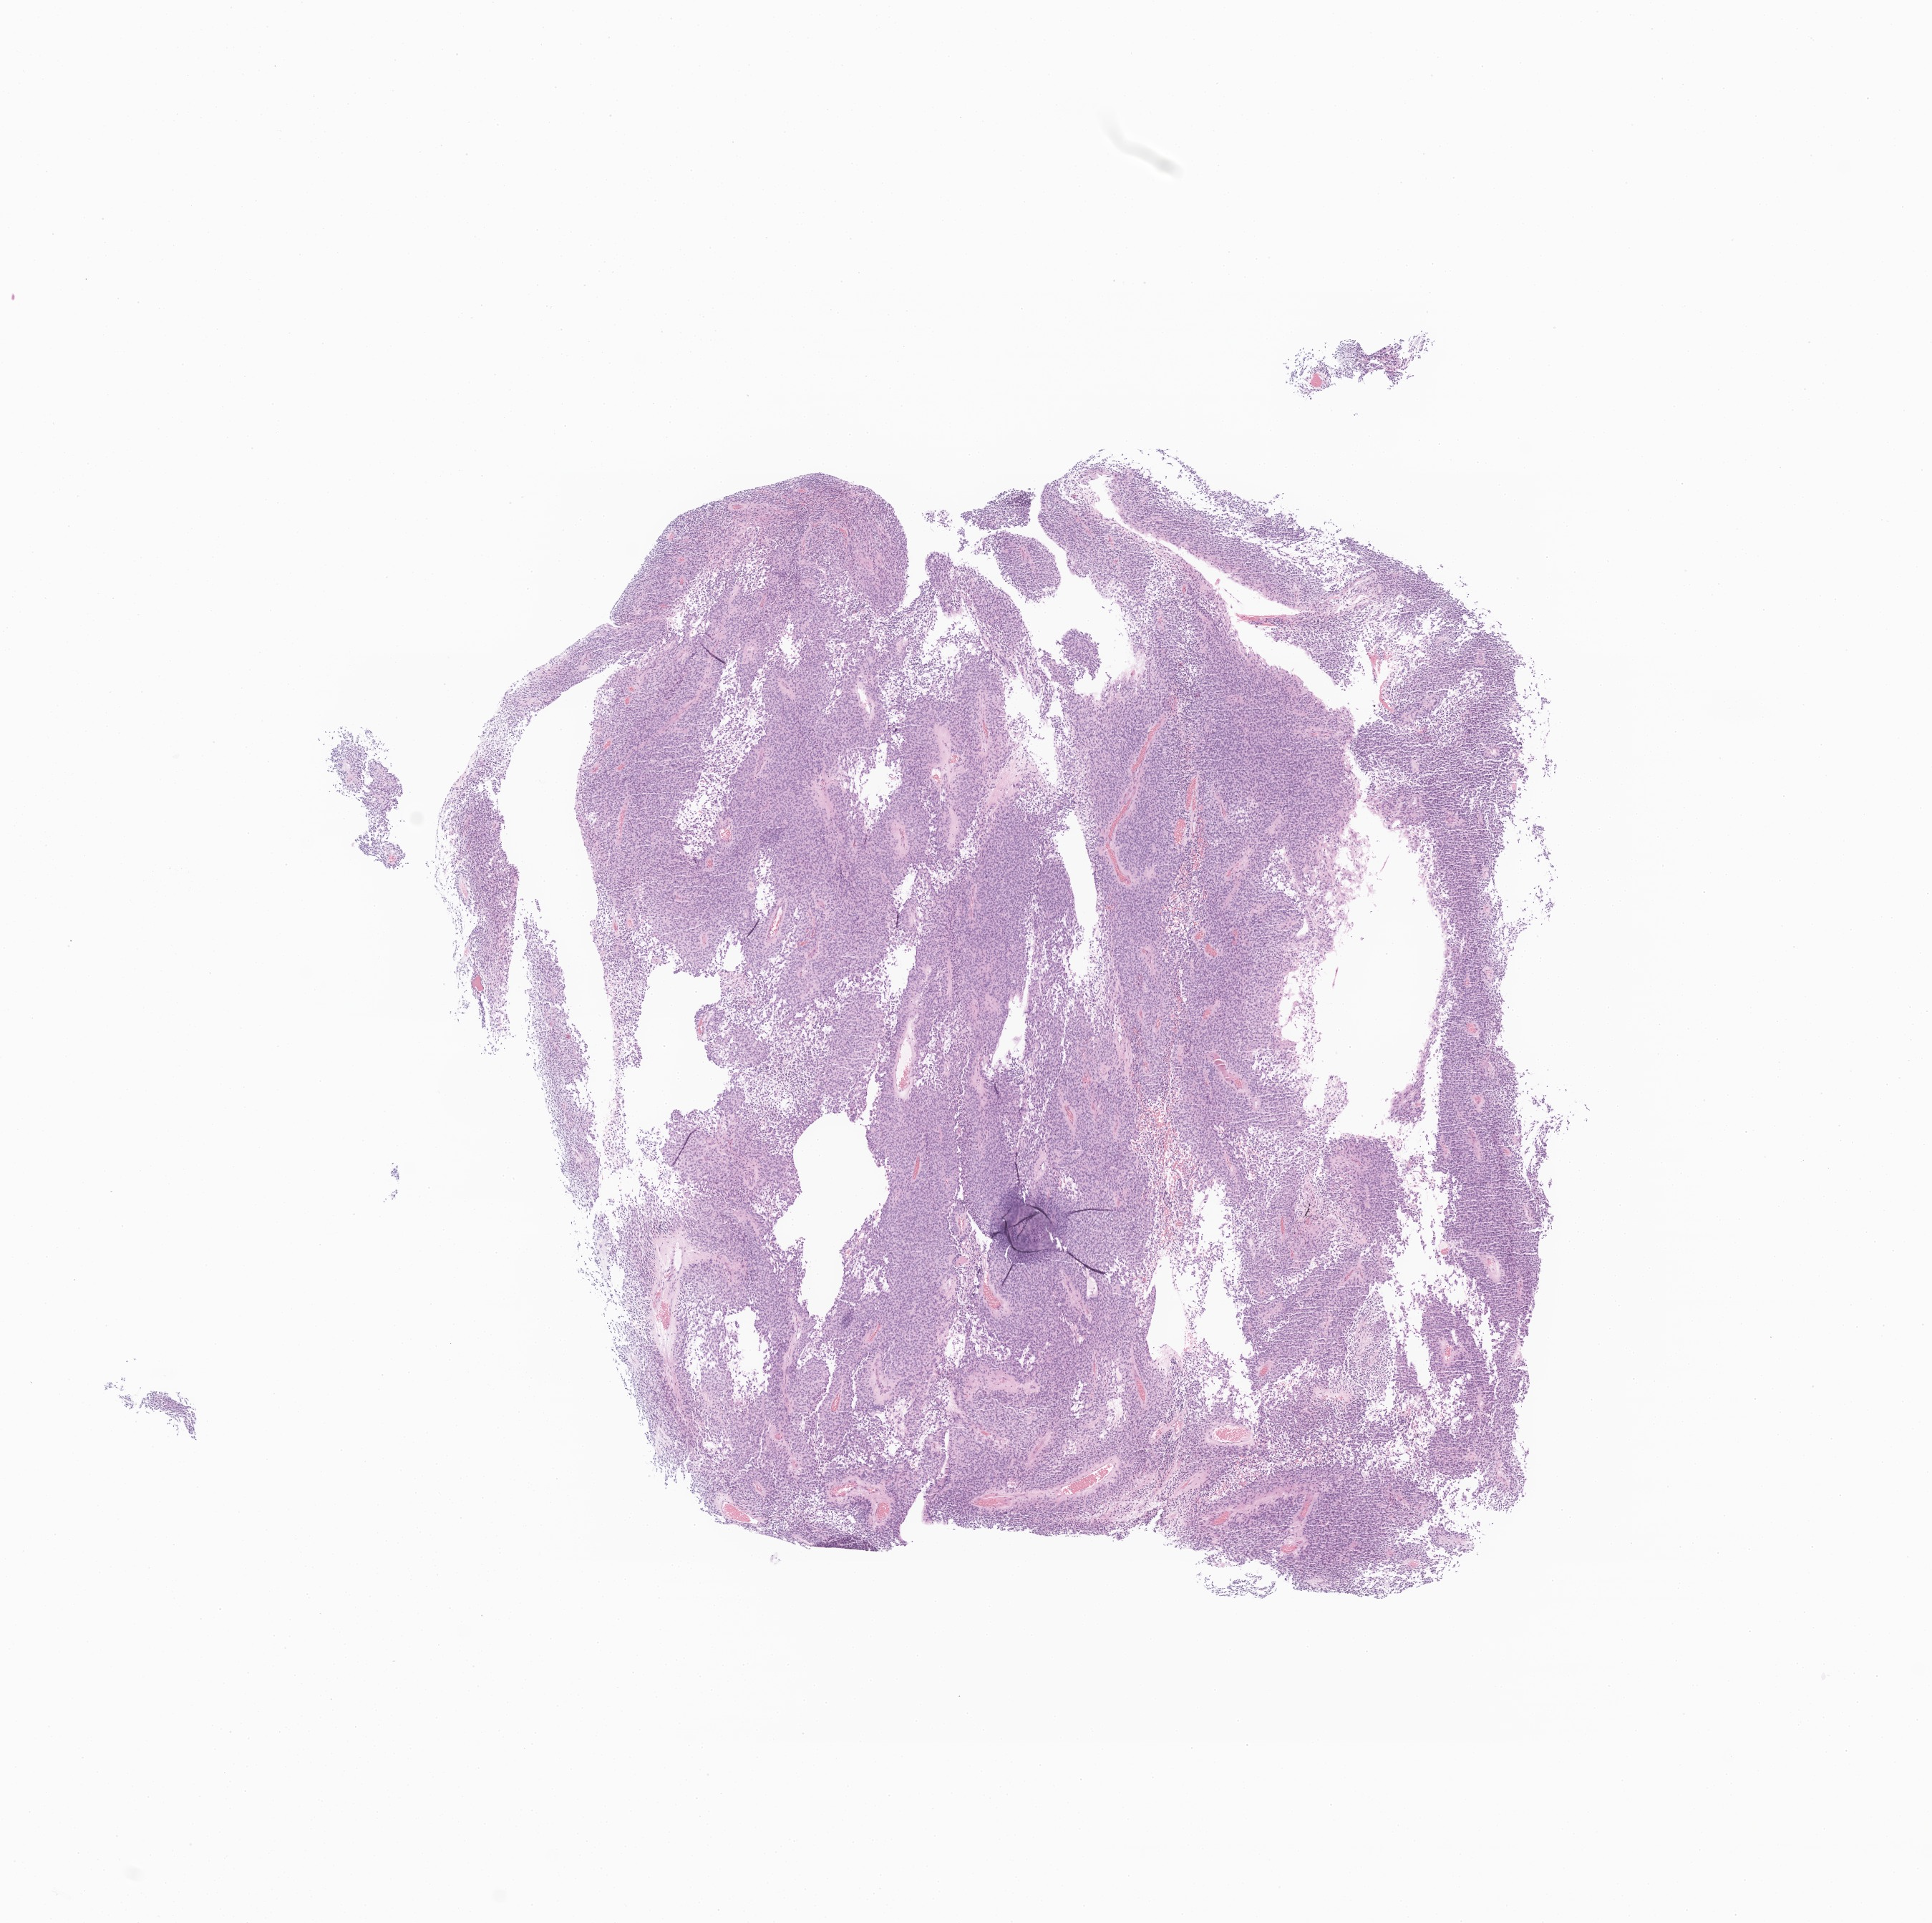
Haematoxylin and eosin whole-slide image of tumor tissue from the brain — low-resolution overview of the scanned area, about 11.4 x 11.3 mm. Formalin-fixed paraffin-embedded section. Patient: female, age 102 months (8 years 6 months).
* recorded diagnosis: Ependymoma, NOS